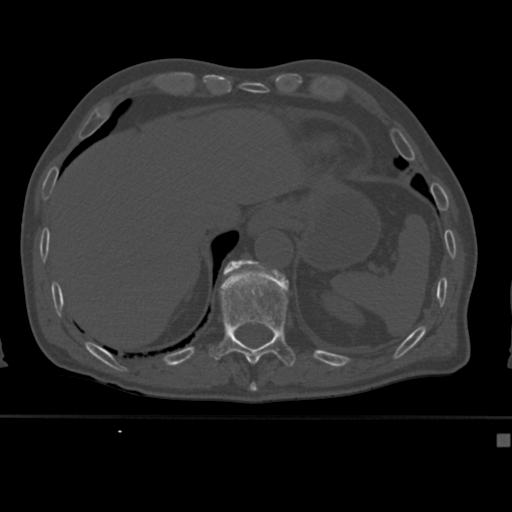
CT including the spine, one axial slice. Position 210 of 430 along the scan axis. Reconstruction kernel Br40s. 120 kVp. Bone window (W 1800 / L 400 HU). 1.5 mm slice thickness. 512 × 512 image matrix. Patient: male, 64 years. Case-level facts recorded for this patient, not image findings: primary cancer: uterus.
Outlined on this slice (semi-automatically segmented with operator editing):
- T11 vertebra: bounding box <209,267,296,367> (left, top, right, bottom; pixels)
- T12 vertebra: <223,260,243,273>